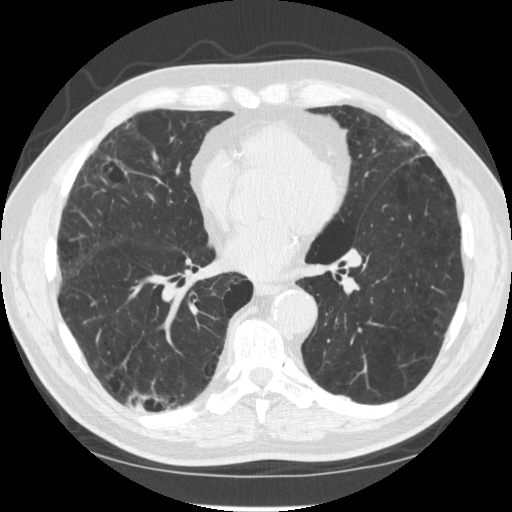
Low-dose screening chest CT, axial slice; second screening round (one year after baseline); lung window (W 1500 / L -600 HU); 1.25 mm slice thickness; standard (soft-tissue) reconstruction kernel (STANDARD); 512 × 512 image matrix, field of view 360 × 360 mm. Male participant, aged 70 years at enrolment. Former smoker at enrolment.
• Expert-annotated lung lesion, bounding box [x1, y1, x2, y2] px = [121, 375, 172, 433].
• The screening reader recorded 2 non-calcified nodules or masses ≥4 mm on this exam; which of them this box marks is not recorded.
• Lung cancer was diagnosed 617 days after this screen: squamous cell carcinoma, NOS, right upper lobe, poorly differentiated (G3), stage IV (AJCC 6th edition).